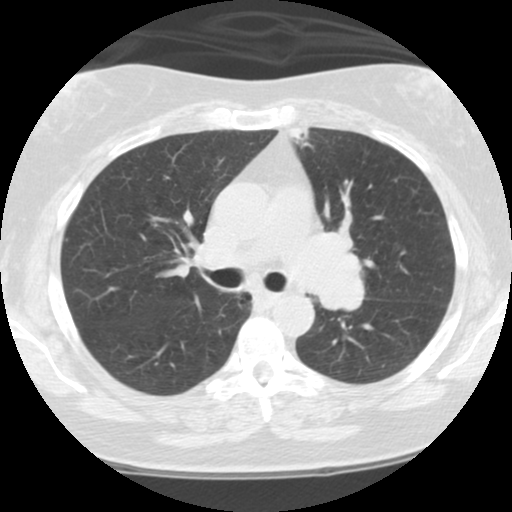
Low-dose screening chest CT, one axial slice. Slice 69 of 108 in the series (ordered by position). Reconstruction kernel STANDARD. Lung window (W 1500 / L -600 HU). 2.5 mm slice thickness. 512 × 512 image matrix.
Outlined on this slice (manually delineated by an expert):
- lesion 1 (tumor, hilum of left lung): bounding box [x1, y1, x2, y2] px = [290, 232, 366, 311]